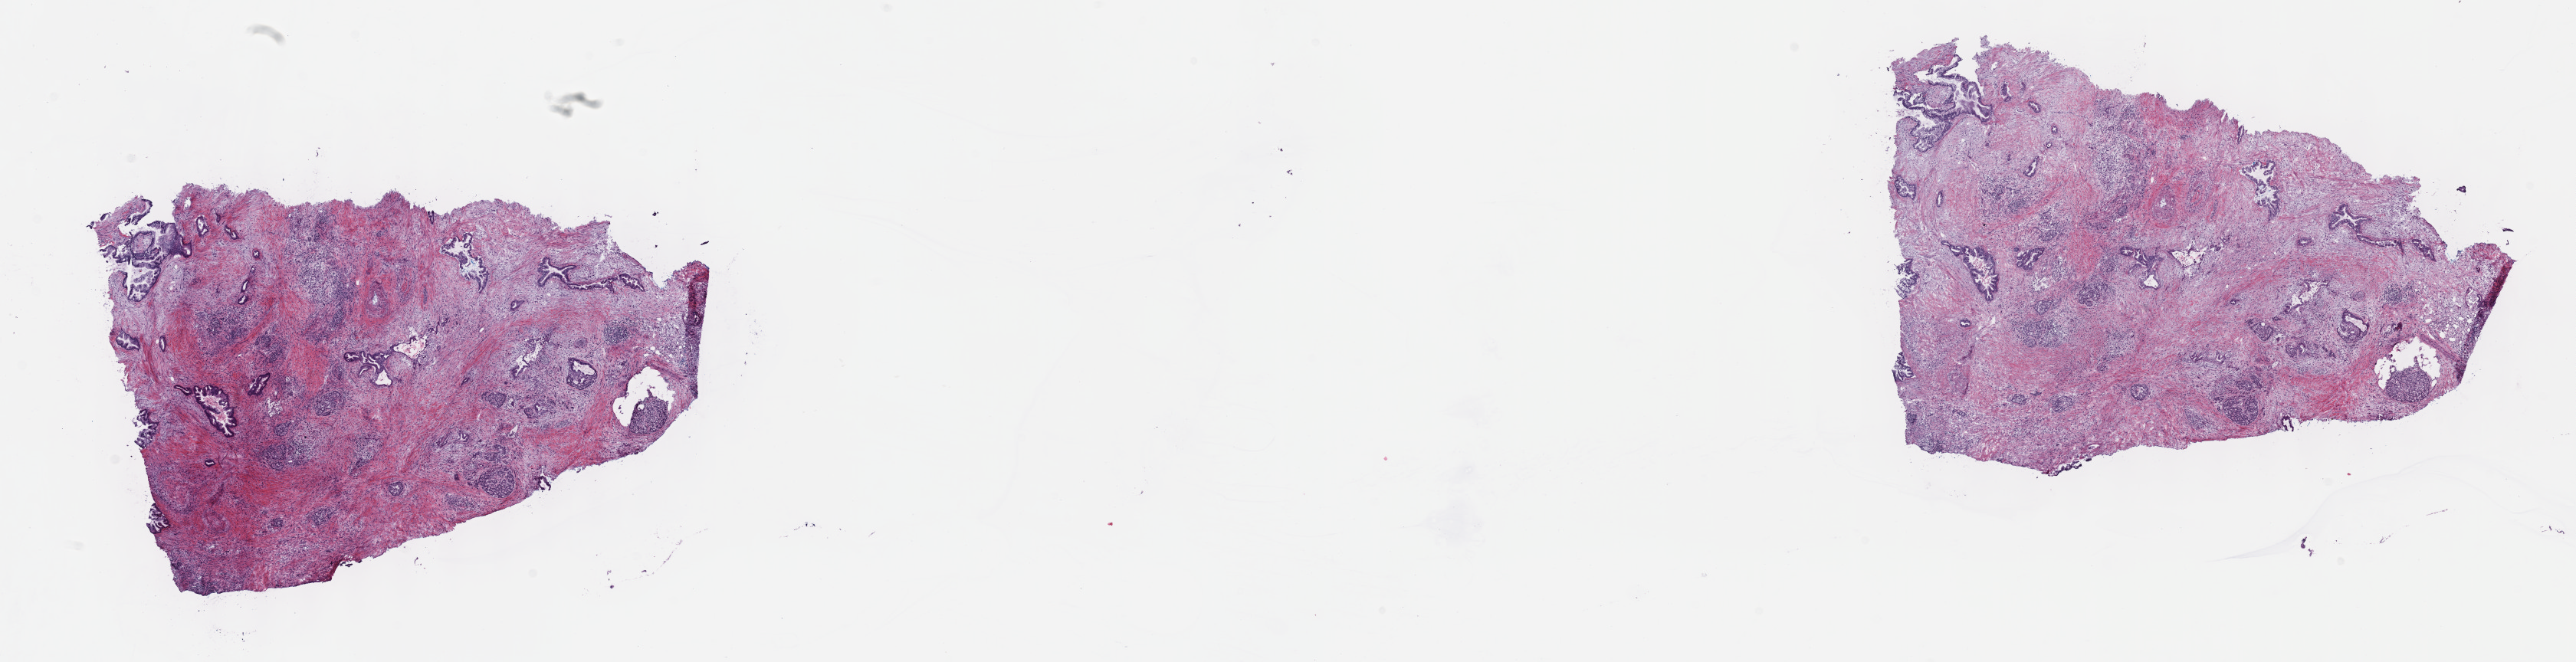
Hematoxylin and eosin (H&E) stained whole-slide image, shown as a low-resolution overview of the whole scanned area (about 27.2 x 7.0 mm, slide scanned at 40x), frozen section, sample: primary tumour, pancreas. Male, age 59 years at initial diagnosis. Histologic grade: G2 (moderately differentiated). Slide review estimates, as recorded: tumour cells 10%, tumour nuclei 15%, normal cells 20%, stromal cells 70%, necrosis 0%. Infiltration values recorded for this section: lymphocyte infiltration 0%, monocyte infiltration 0%, neutrophil infiltration 0%.
AJCC pathologic stage: IIB (7th edition). Diagnosis: Infiltrating duct carcinoma, NOS. Lymph nodes positive (case pathology): 4 of 17 examined.